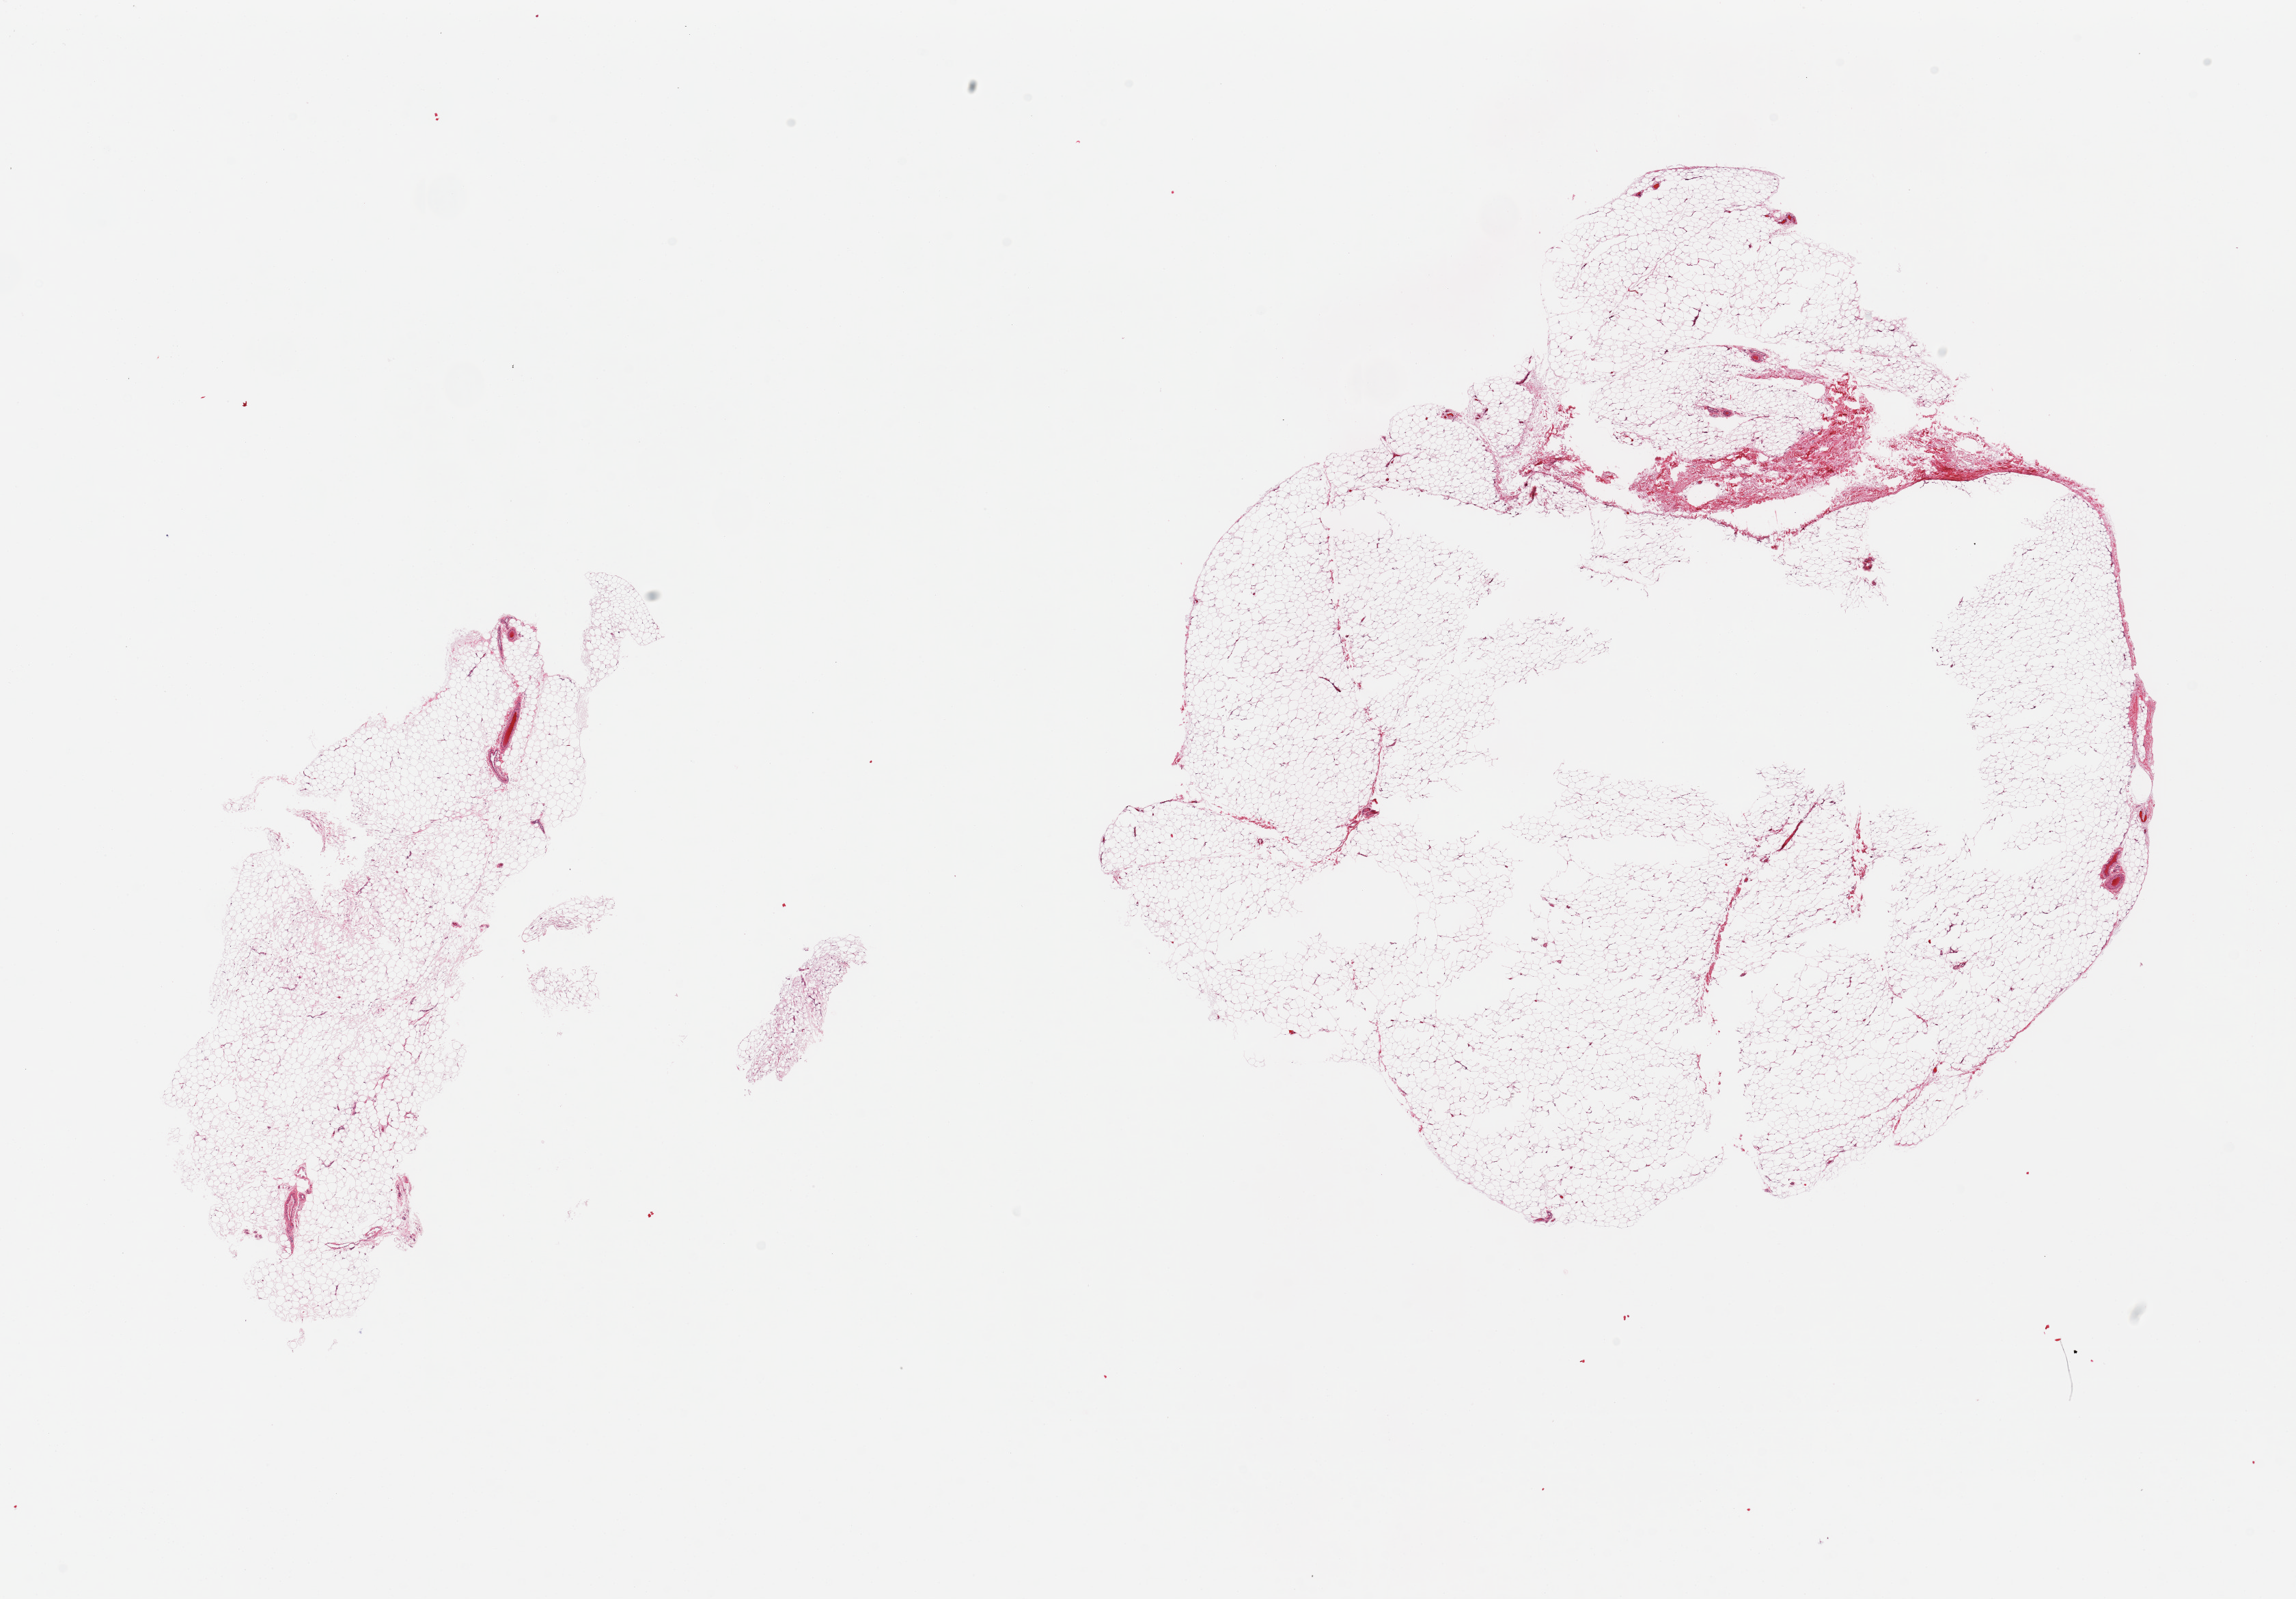
Whole-slide image, haematoxylin and eosin stain, brightfield, low-resolution overview of the scanned area, about 26.6 x 18.5 mm; PAXgene-fixed paraffin-embedded (PFPE) section; sampled site (target tissue): adipose tissue; donor tissue sample. Male donor.
Reviewer comment on this tissue sample: 2 pieces; large central defect in one (?poor fixation), <10% fibrous tissue.